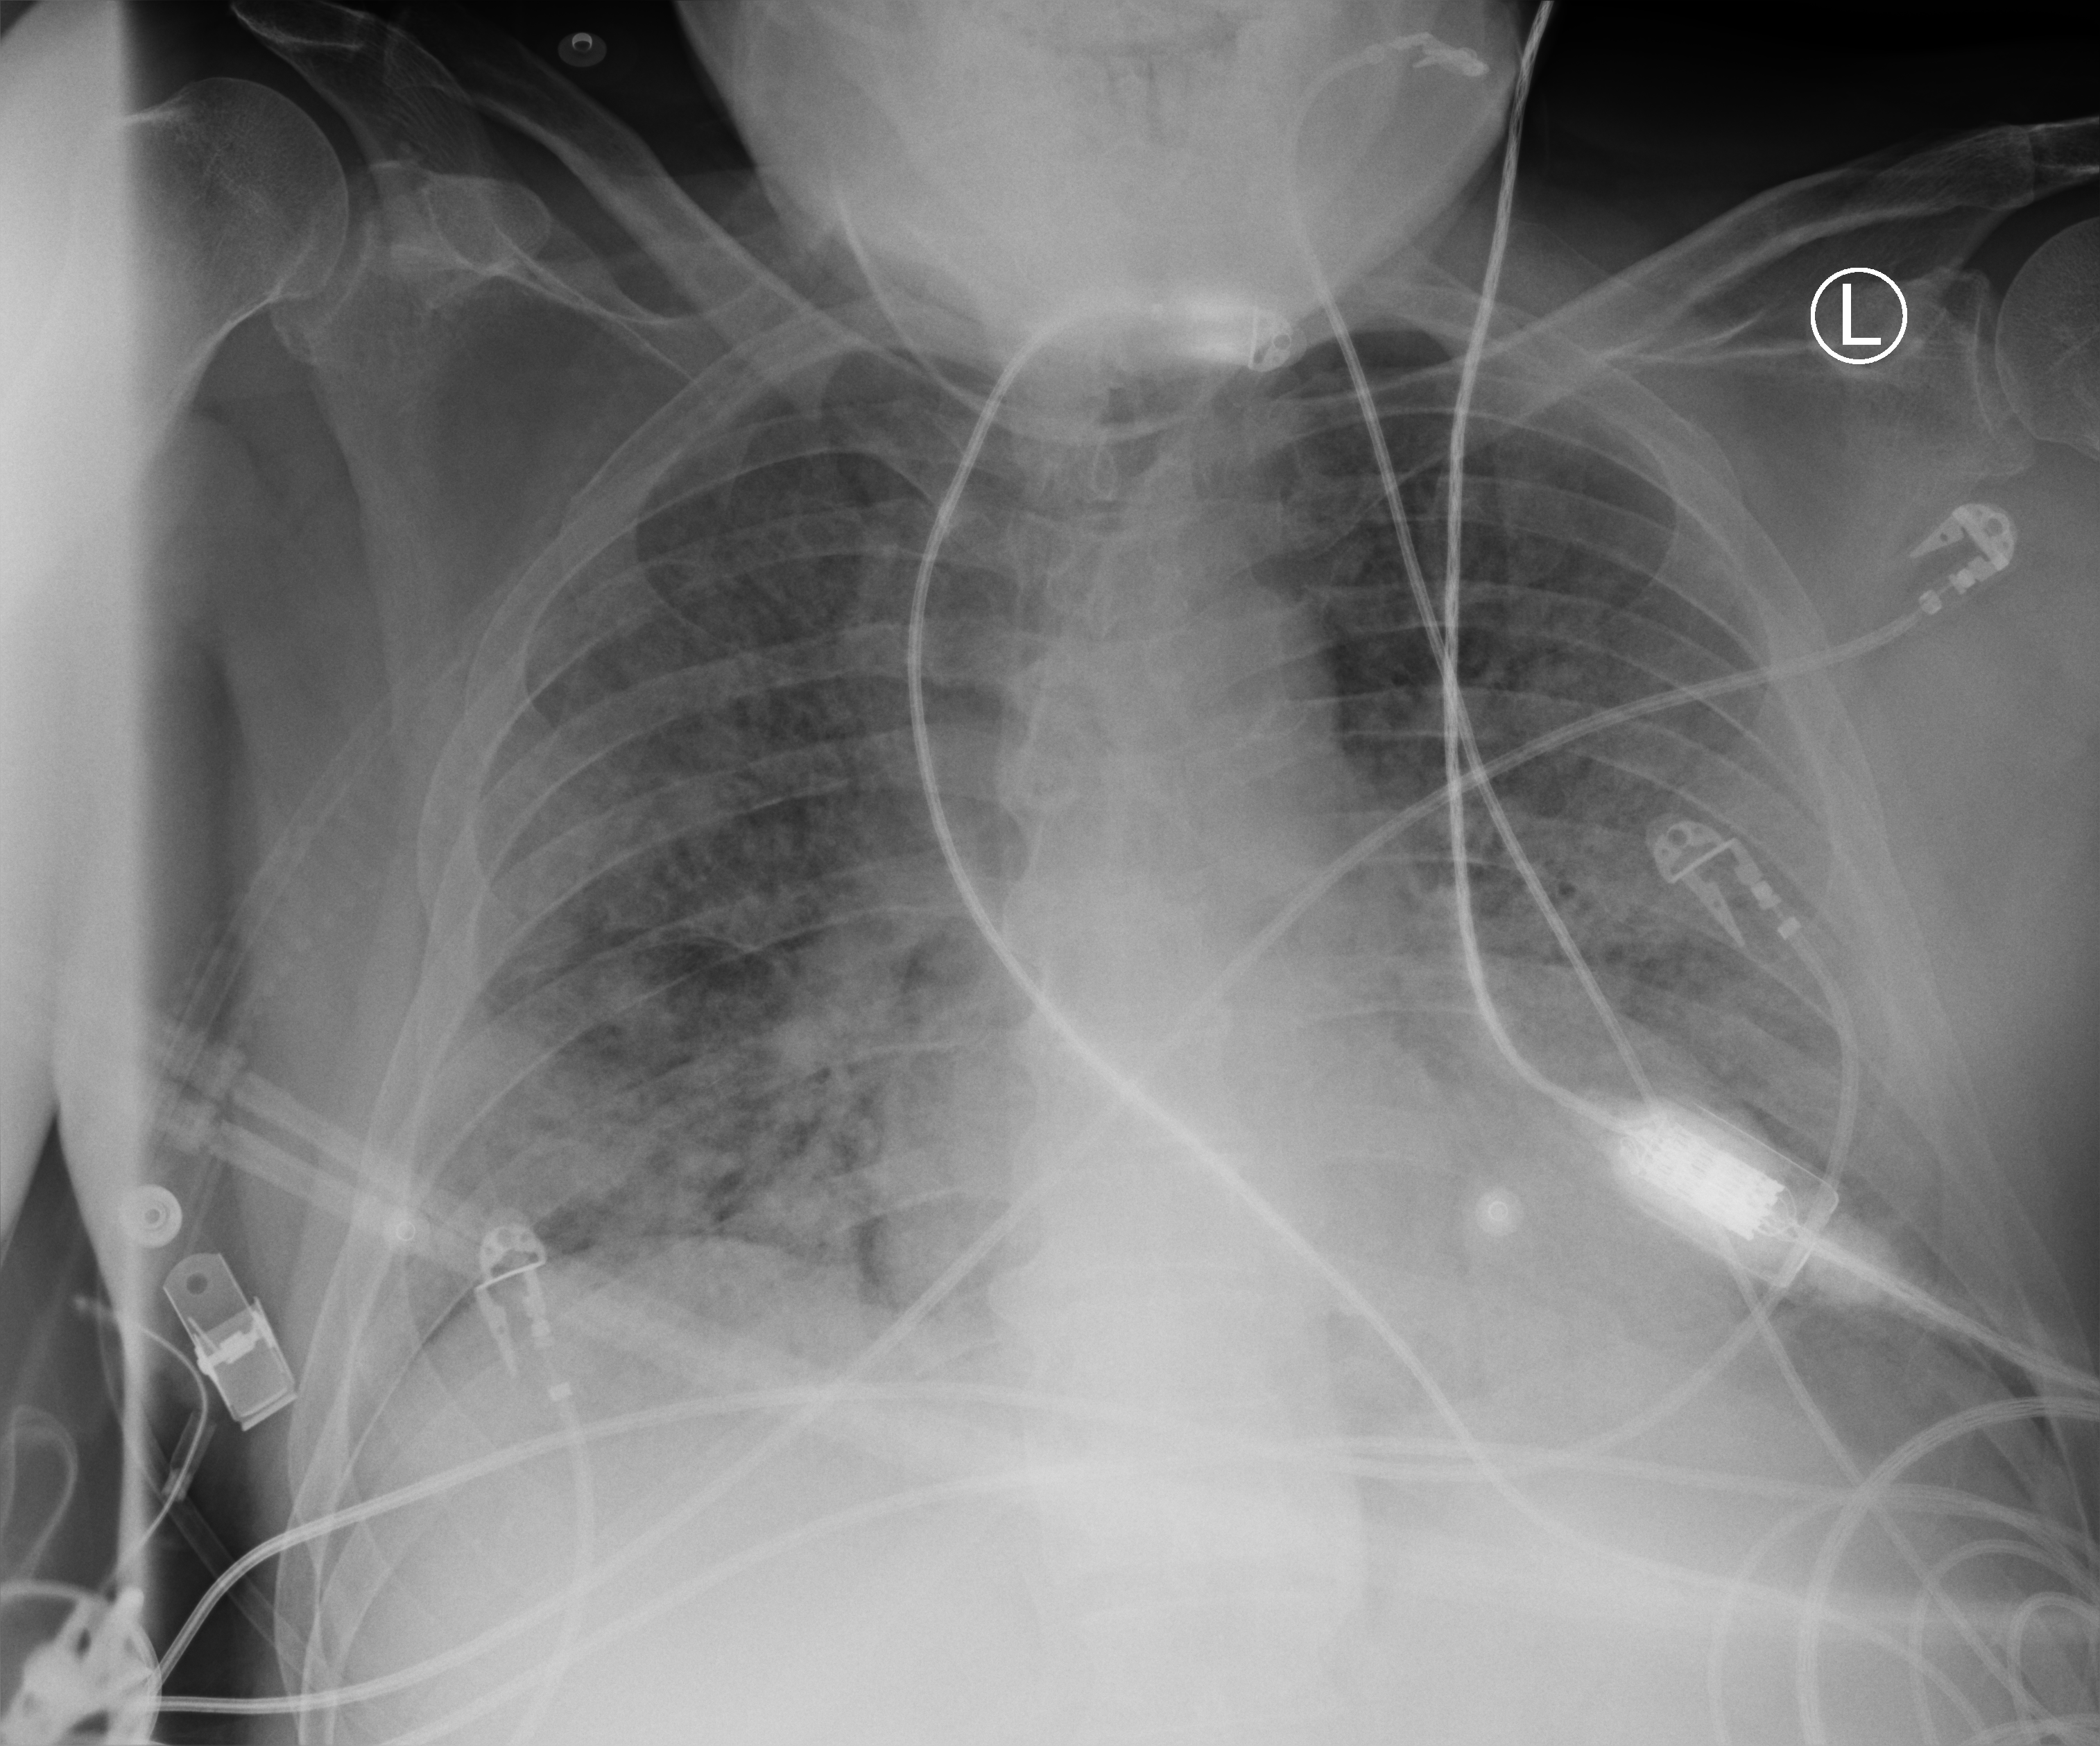
Chest X-ray (portable), anteroposterior (AP) projection. Patient hospitalised with COVID-19; male, aged 60–74 years.
Admission-level facts for this patient (not findings on this image; timing relative to this image not recorded): mechanically ventilated during this hospital stay: yes; admitted to intensive care during this hospital stay: yes.